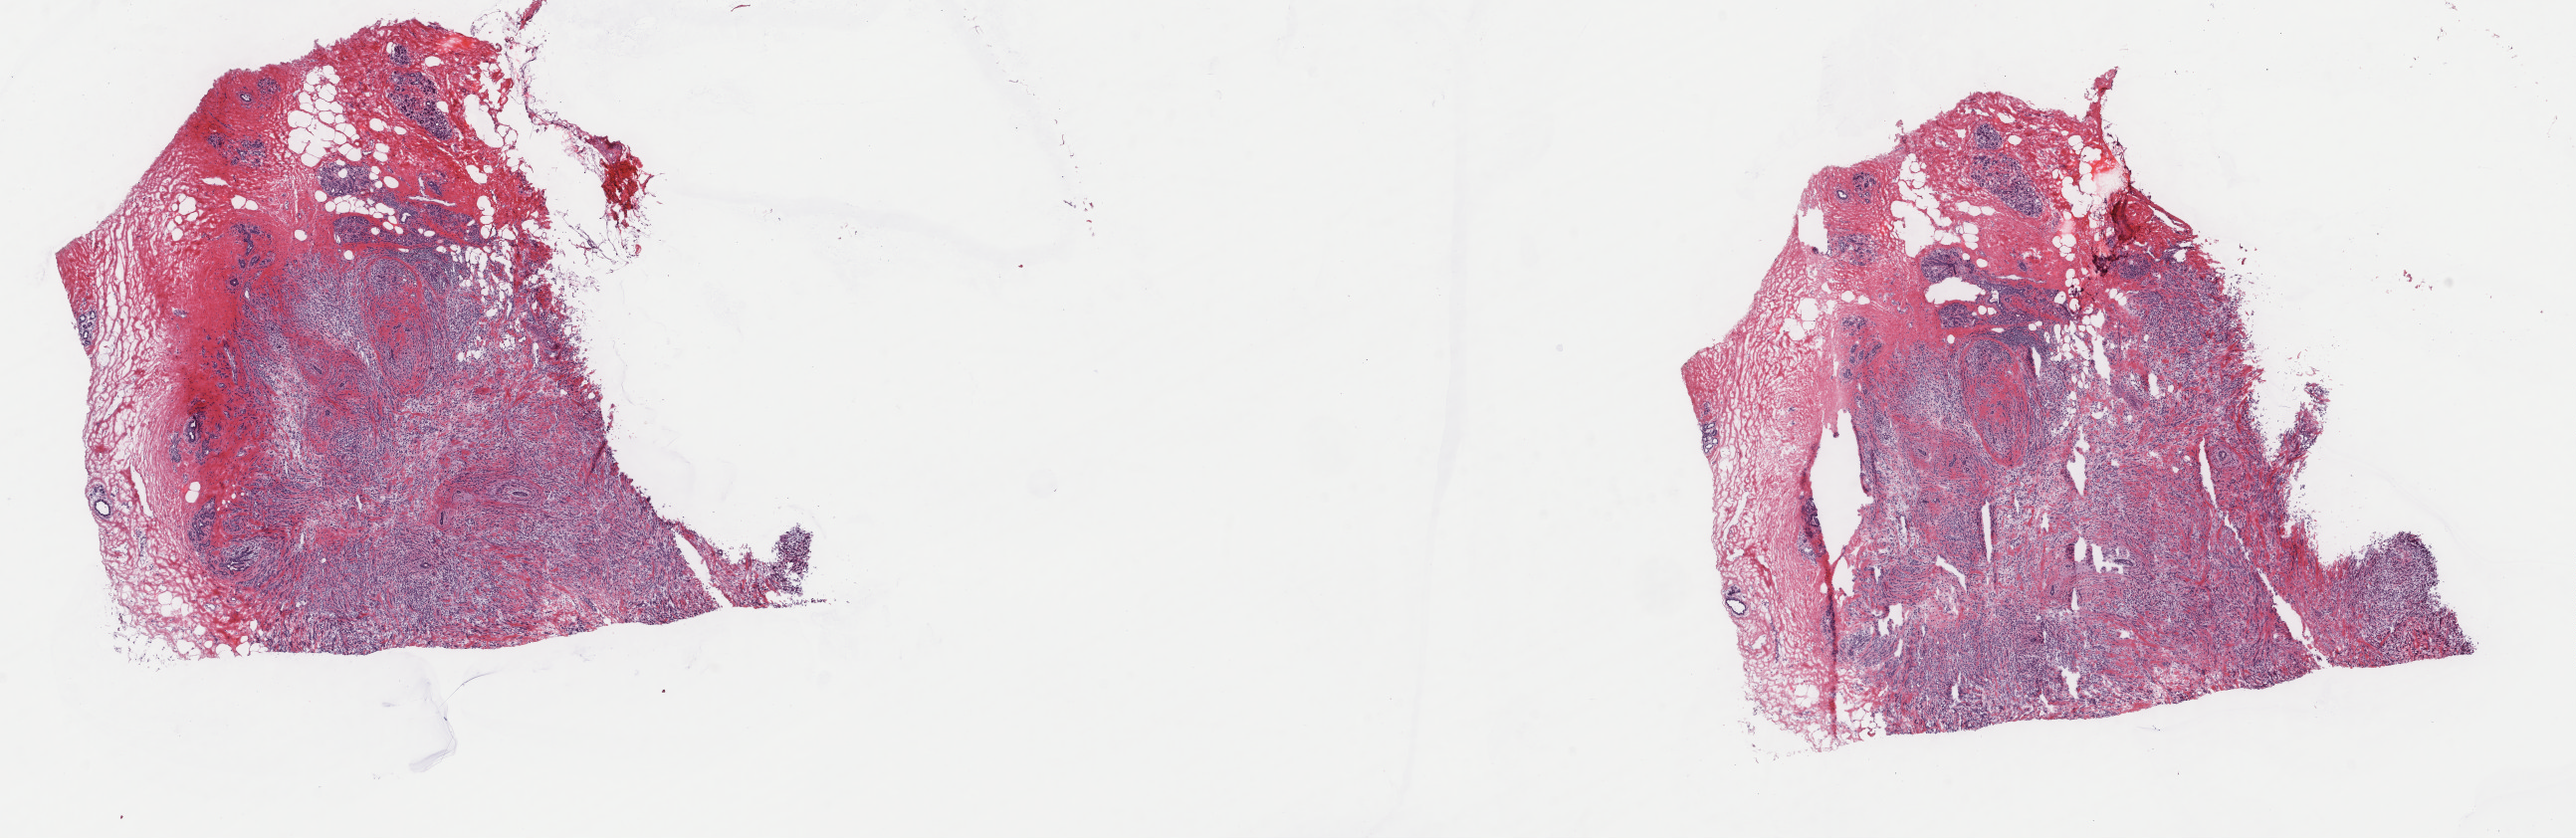
H&E whole-slide image — a low-resolution overview of the entire scanned area, about 20.5 x 6.7 mm (from a 40x scan), frozen section from the top of the tissue portion, sample: primary tumour, breast. Patient: female, age at initial diagnosis 54 years. Composition of this section per pathologist review: tumour cells 80%, tumour nuclei 80%, normal cells 0%, stromal cells 20%, necrosis 0%. Infiltration values recorded for this section: lymphocyte infiltration 40%, monocyte infiltration 20%, neutrophil infiltration 20%.
Laterality: left. Diagnosis: Lobular carcinoma, NOS. AJCC pathologic stage: IIB. TNM: T2 N1 M0.